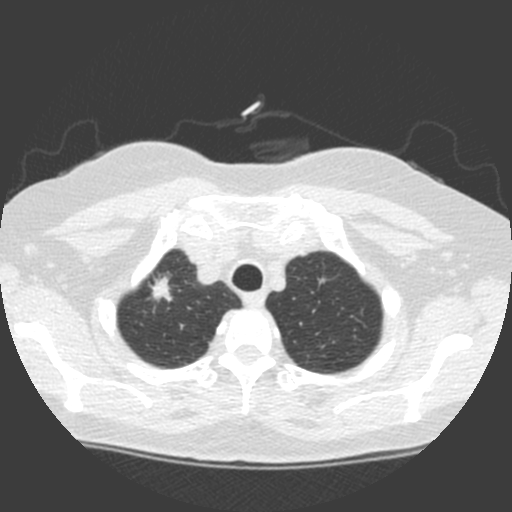
Low-dose screening chest CT, one axial slice; position 140 of 155 along the scan axis; 120 kVp; lung window (W 1500 / L -600 HU); 2 mm slice thickness; 512 × 512 image matrix, field of view 314 × 314 mm.
Annotated regions visible in this slice (manually delineated by an expert):
- lesion 1 (tumor, upper lobe of right lung): bounding box (x1, y1, x2, y2) in pixels: (149, 276, 172, 302)